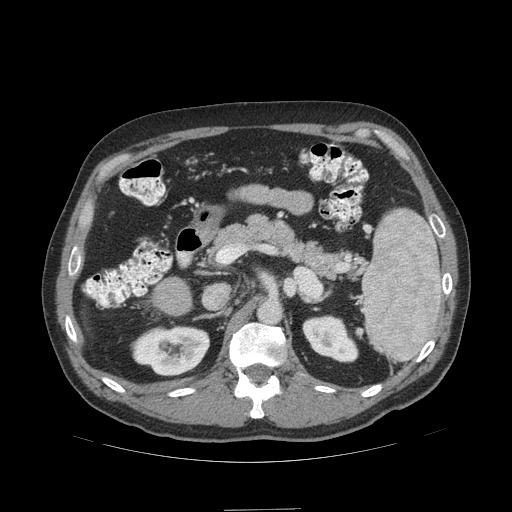
Contrast-enhanced abdominal CT (liver protocol), one axial slice. Slice 55 of 99 in the series (ordered by position). Reconstruction kernel STANDARD. Soft-tissue window (W 400 / L 40 HU). 2.5 mm slice thickness. 512 × 512 image matrix, field of view 440 × 440 mm. From the clinical record (not read from this slice): diagnosis: hepatocellular carcinoma (patient treated with transarterial chemoembolisation; whether this scan precedes or follows treatment is not stated here); TNM stage (as recorded): Stage-I.
Structures marked on this image (semi-automatic segmentation, software-assisted and operator-edited):
- liver parenchyma outside the tumour (the mass and vessels are separate outlines, so this box may not span the whole liver): box from (x=82, y=311) to (x=85, y=314) px